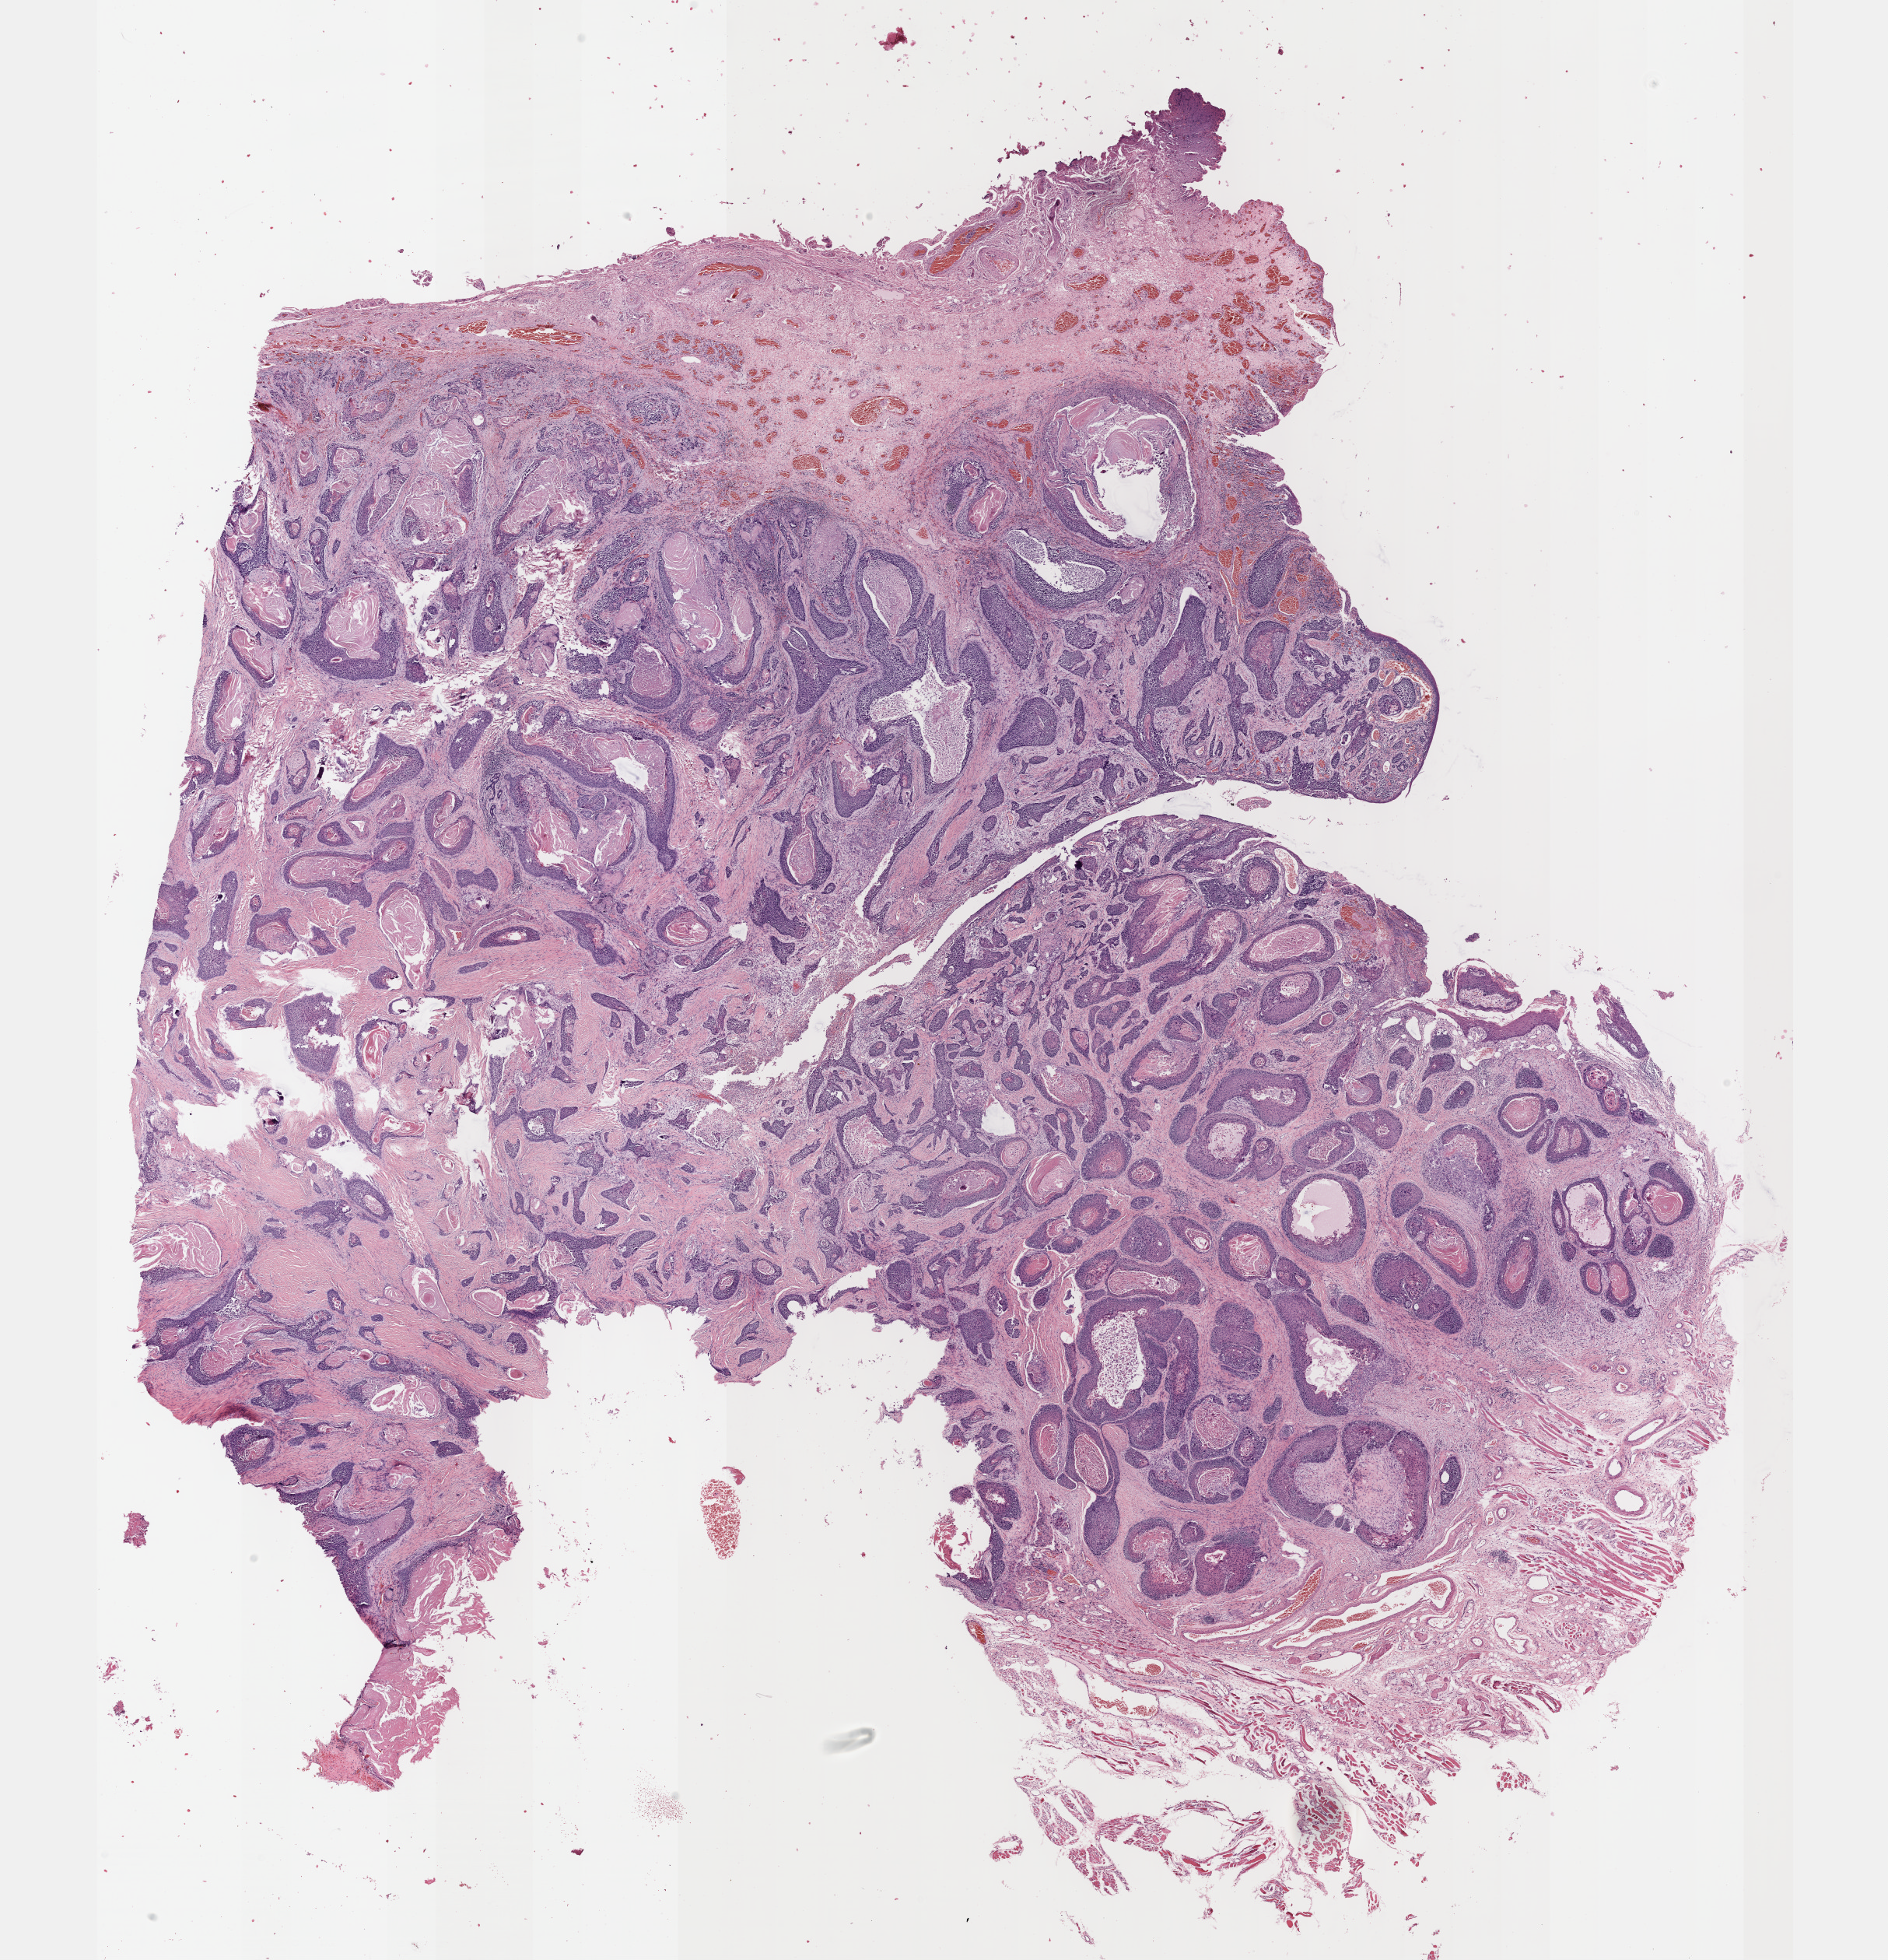
Digitized Hematoxylin and eosin (H&E) stained tissue section (whole slide), low-resolution overview of the scanned area, about 19.6 x 20.4 mm (acquisition: 40x scan); FFPE section; sample: primary tumour, head and neck. Male patient; age at initial diagnosis 67 years. Histologic grade: G1 (well differentiated).
* AJCC pathologic stage: IVA (7th edition)
* pathologic diagnosis: Squamous cell carcinoma, NOS (floor of mouth, NOS)
* TNM: T4a N2c M0